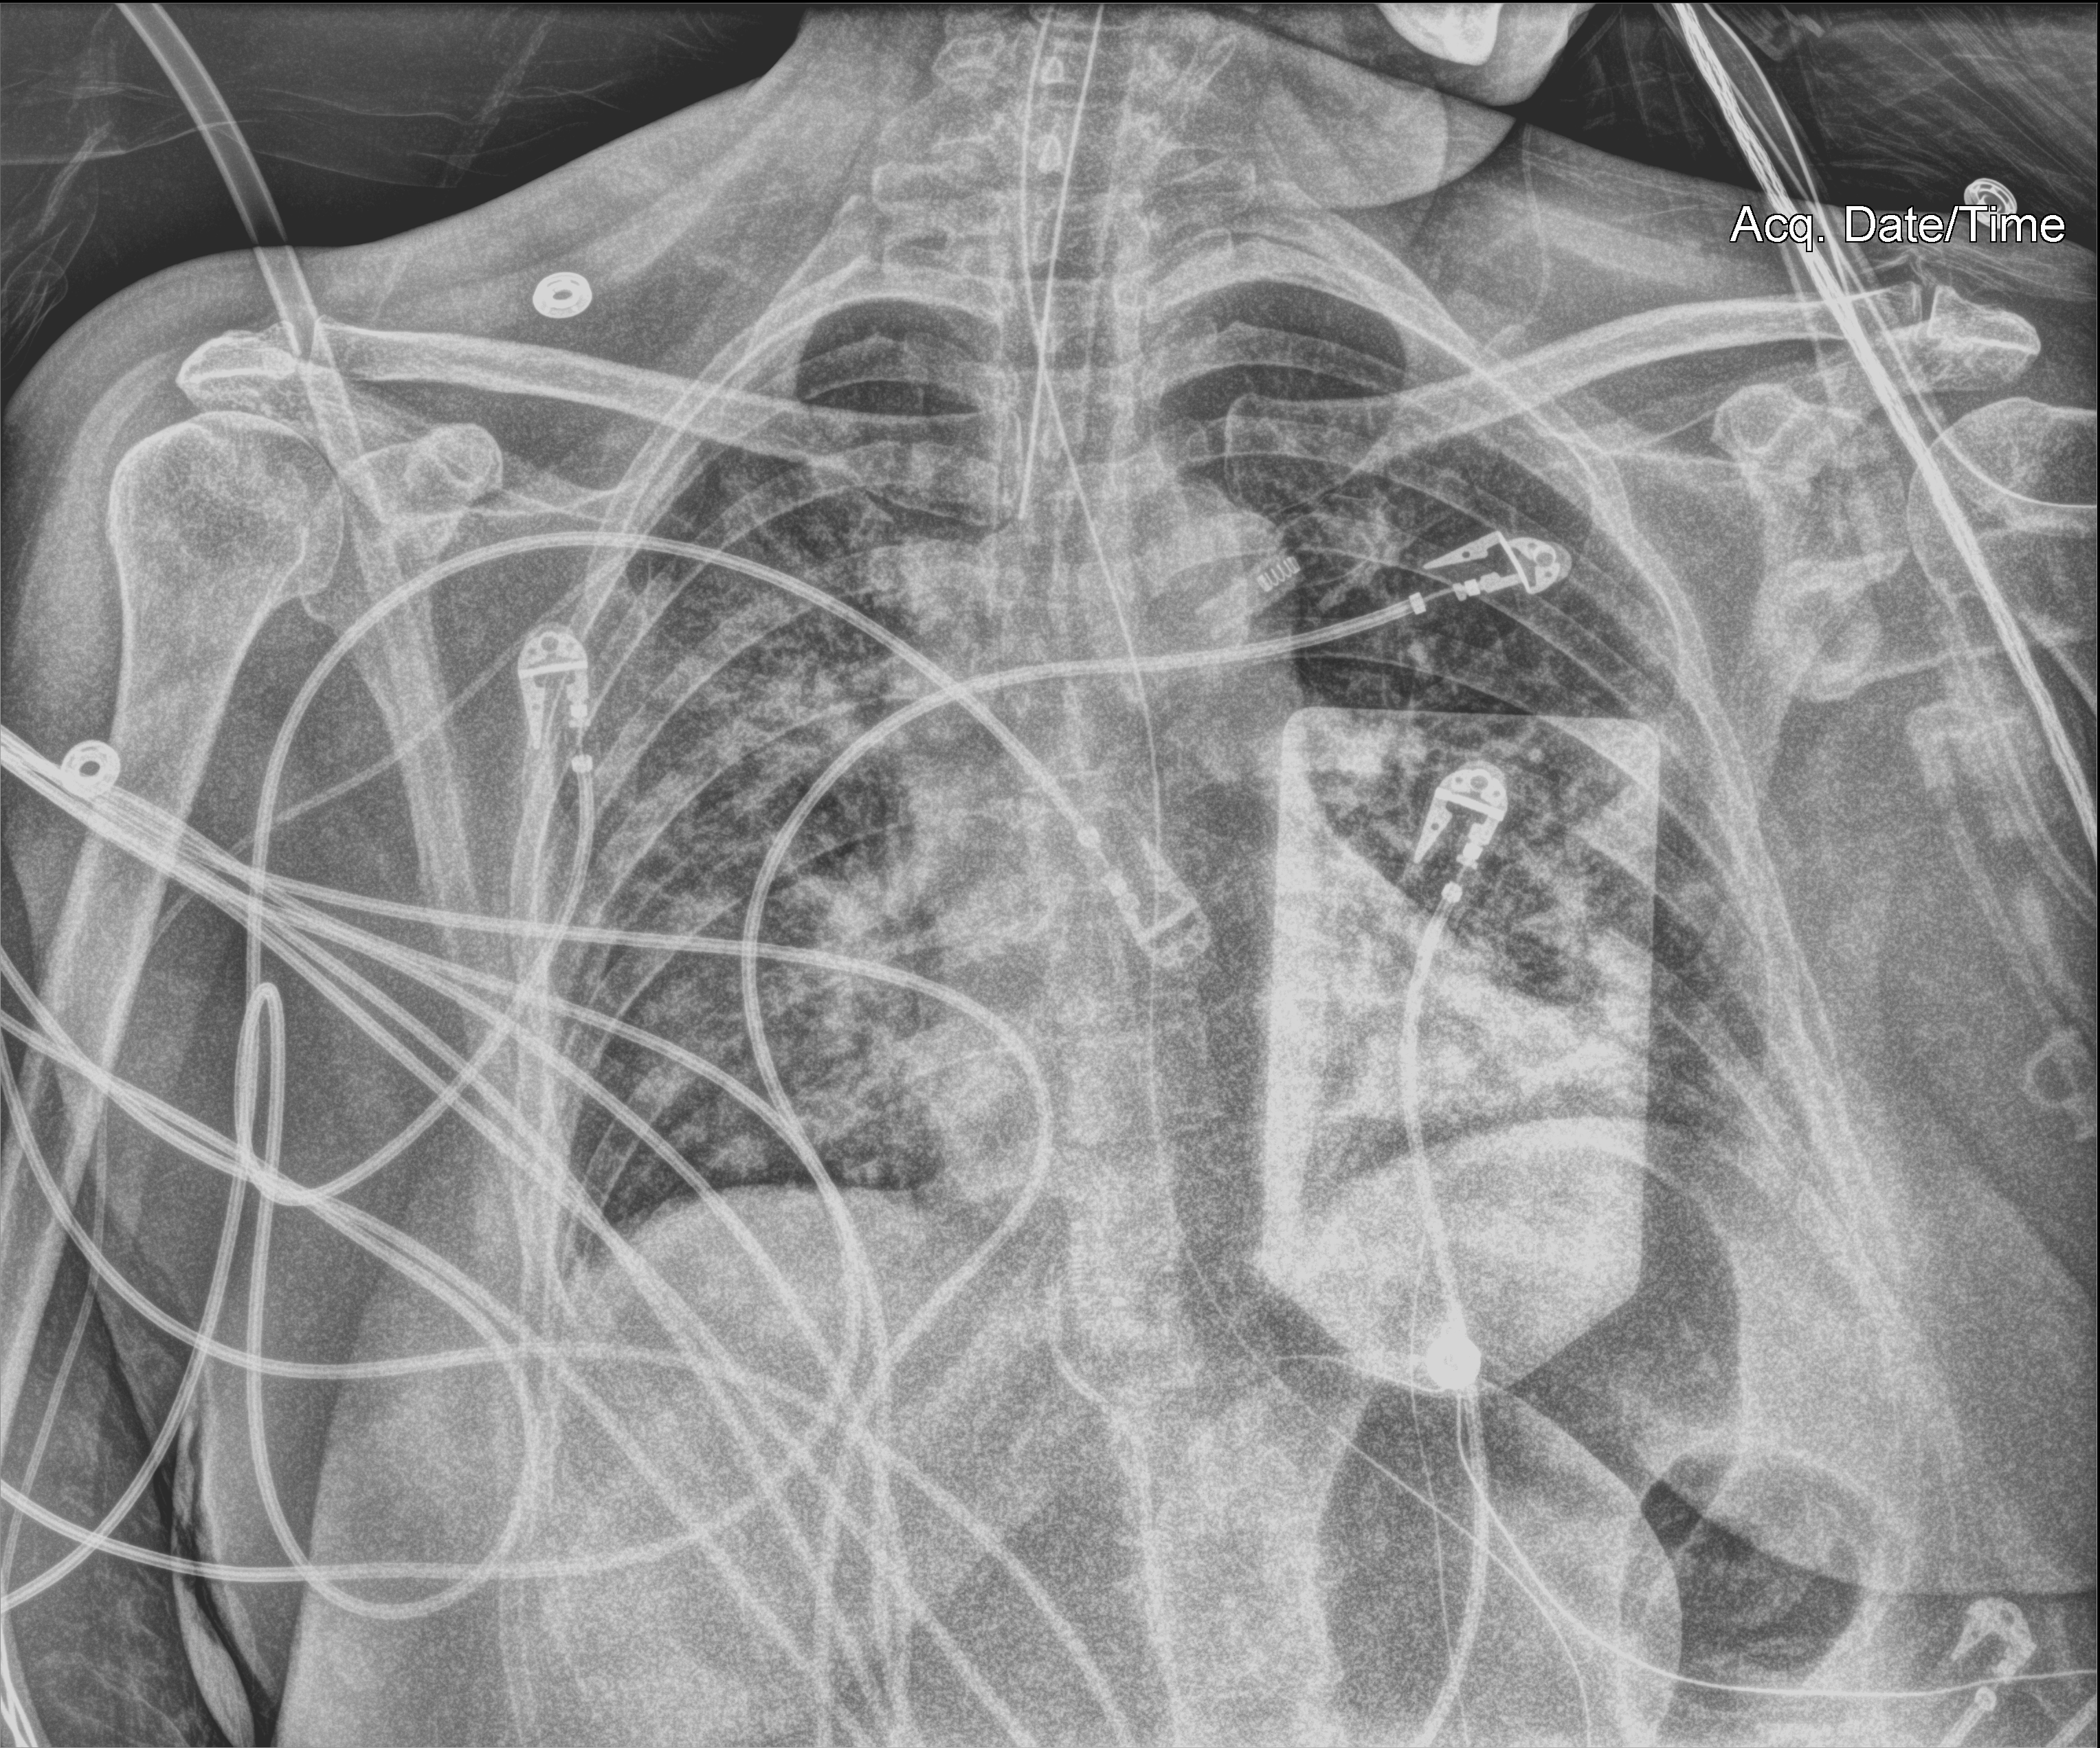
Bedside chest radiograph (computed radiography); anteroposterior (AP) projection. Patient hospitalised with COVID-19; female, aged 18–59 years.
Hospital-stay facts (about this admission, not read from this image; timing relative to this image not recorded): mechanically ventilated during this hospital stay: yes; length of hospital stay: 22 days.